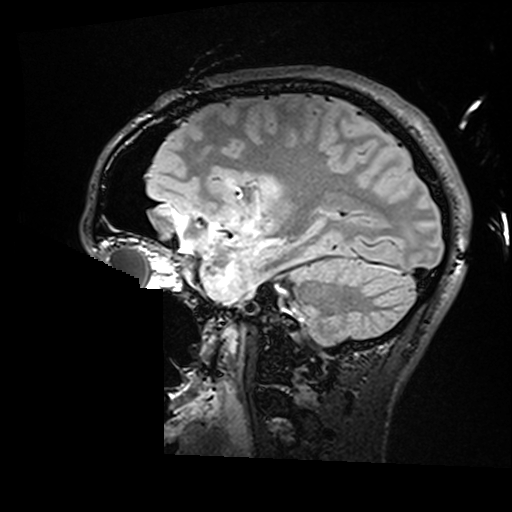
Brain MRI from a brain-tumour surgery series, one sagittal slice; position 110 of 176 along the scan axis; T2 FLAIR; 1 mm slice thickness; 512 × 512 image matrix. From the clinical record (not read from this slice): histopathology: Astrocytoma; WHO grade: 2; IDH mutation: yes.
Annotated regions visible in this slice (expert manual segmentation):
- residual tumour: bounding box (x1, y1, x2, y2) in pixels: (228, 179, 286, 198)